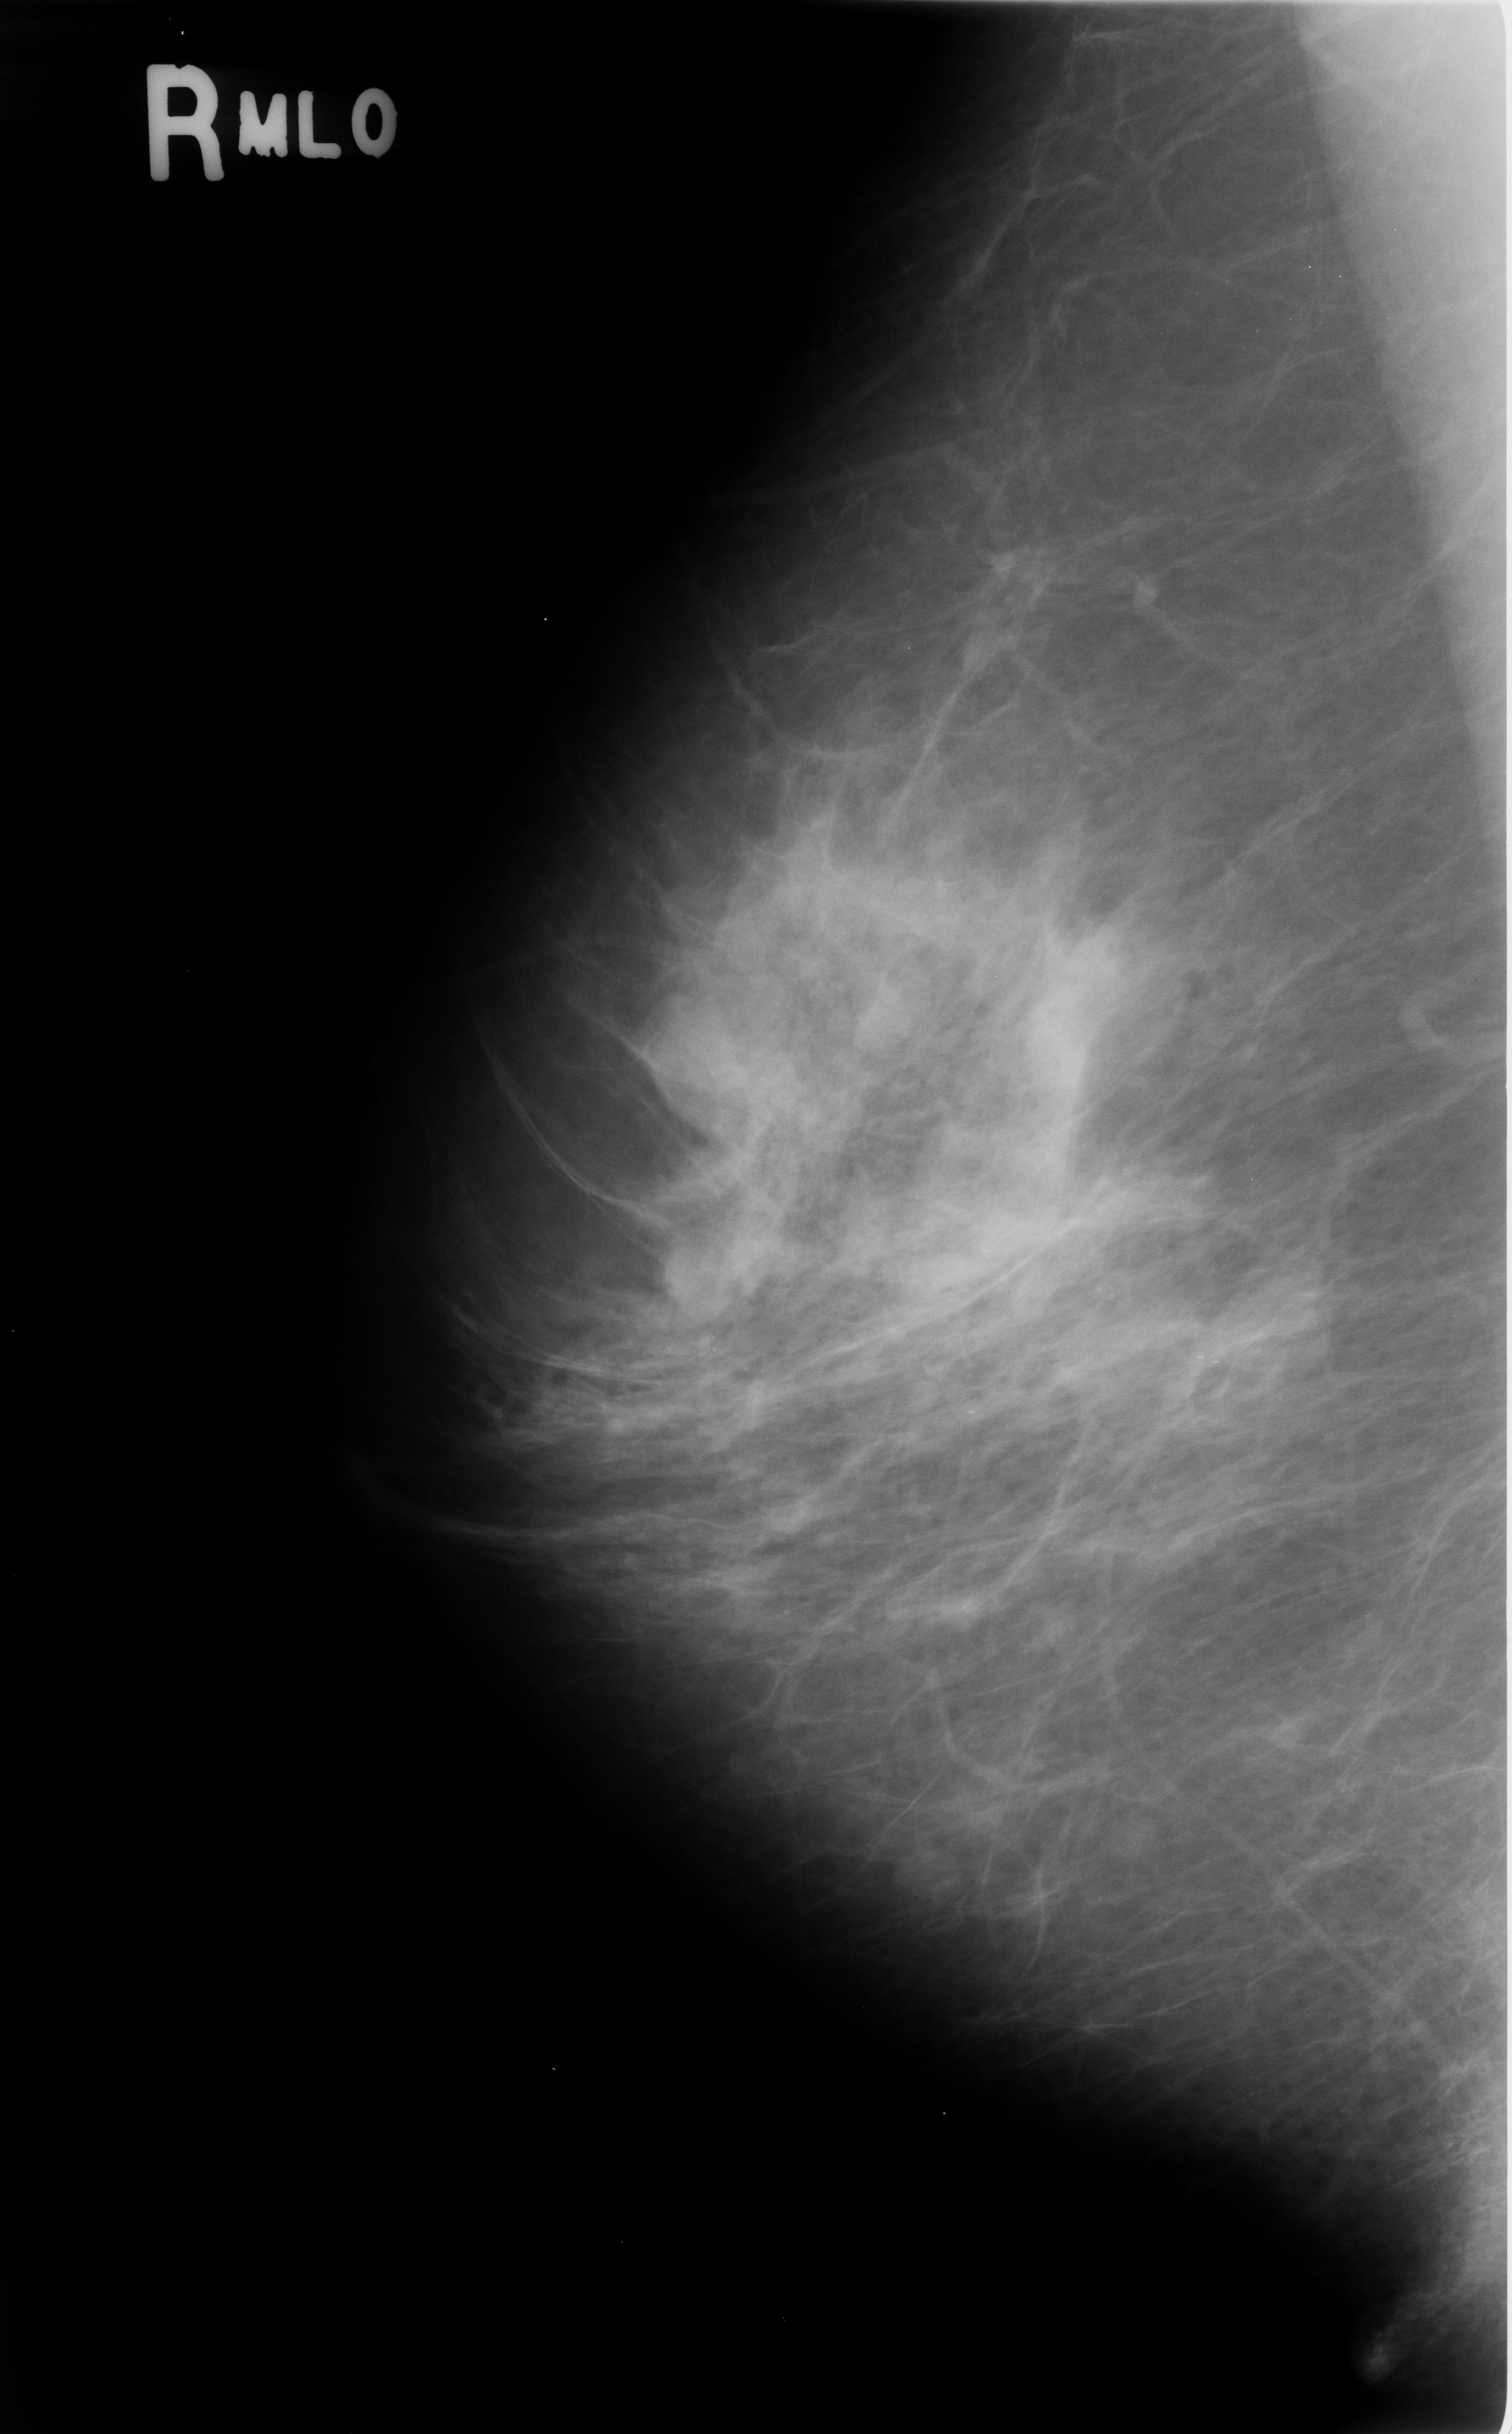
Digitized screen-film mammogram. Right breast. MLO view. Breast composition: scattered fibroglandular densities (BI-RADS density category 2 of 4). 1512 × 2434 image matrix.
Marked abnormalities (boxes around the expert regions of interest):
- mass, shape oval, margins circumscribed; BI-RADS assessment category 4; pathology (as recorded): benign: bounding box (x1, y1, x2, y2) in pixels: (635, 1005, 797, 1143)